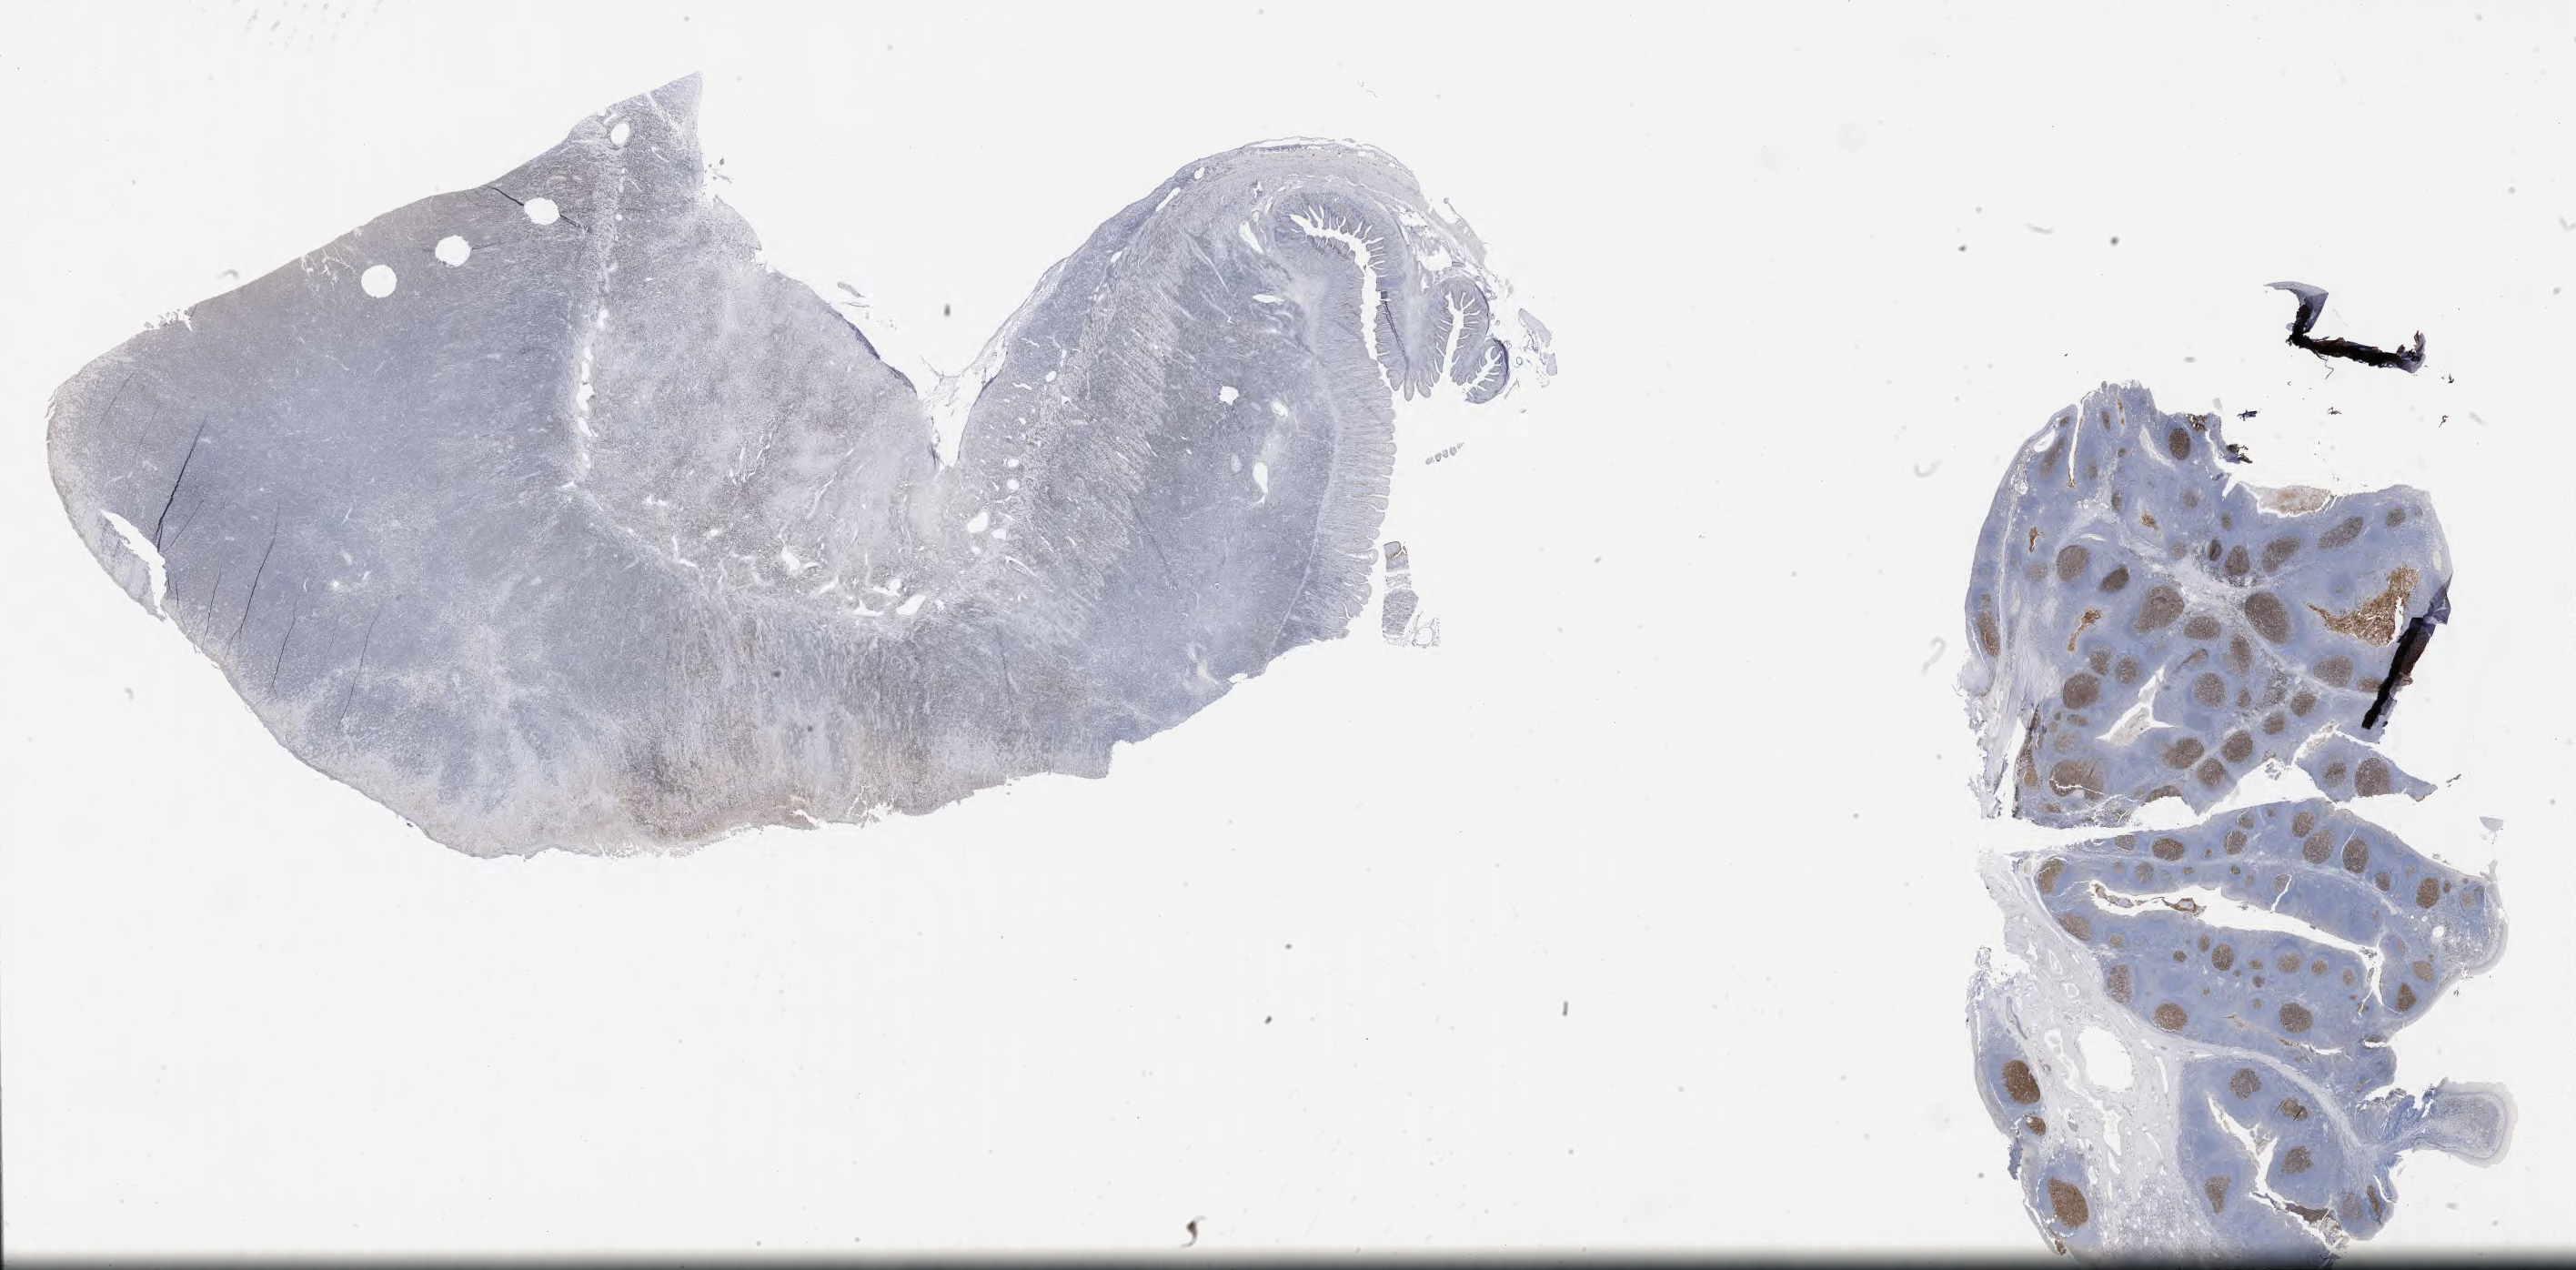
IHC for CD10, whole-slide image — a low-resolution overview of the entire scanned area, about 45.8 x 22.6 mm, tumor tissue. Patient: male, age at initial diagnosis 4 years.
Histologic diagnosis: Burkitt lymphoma, NOS.